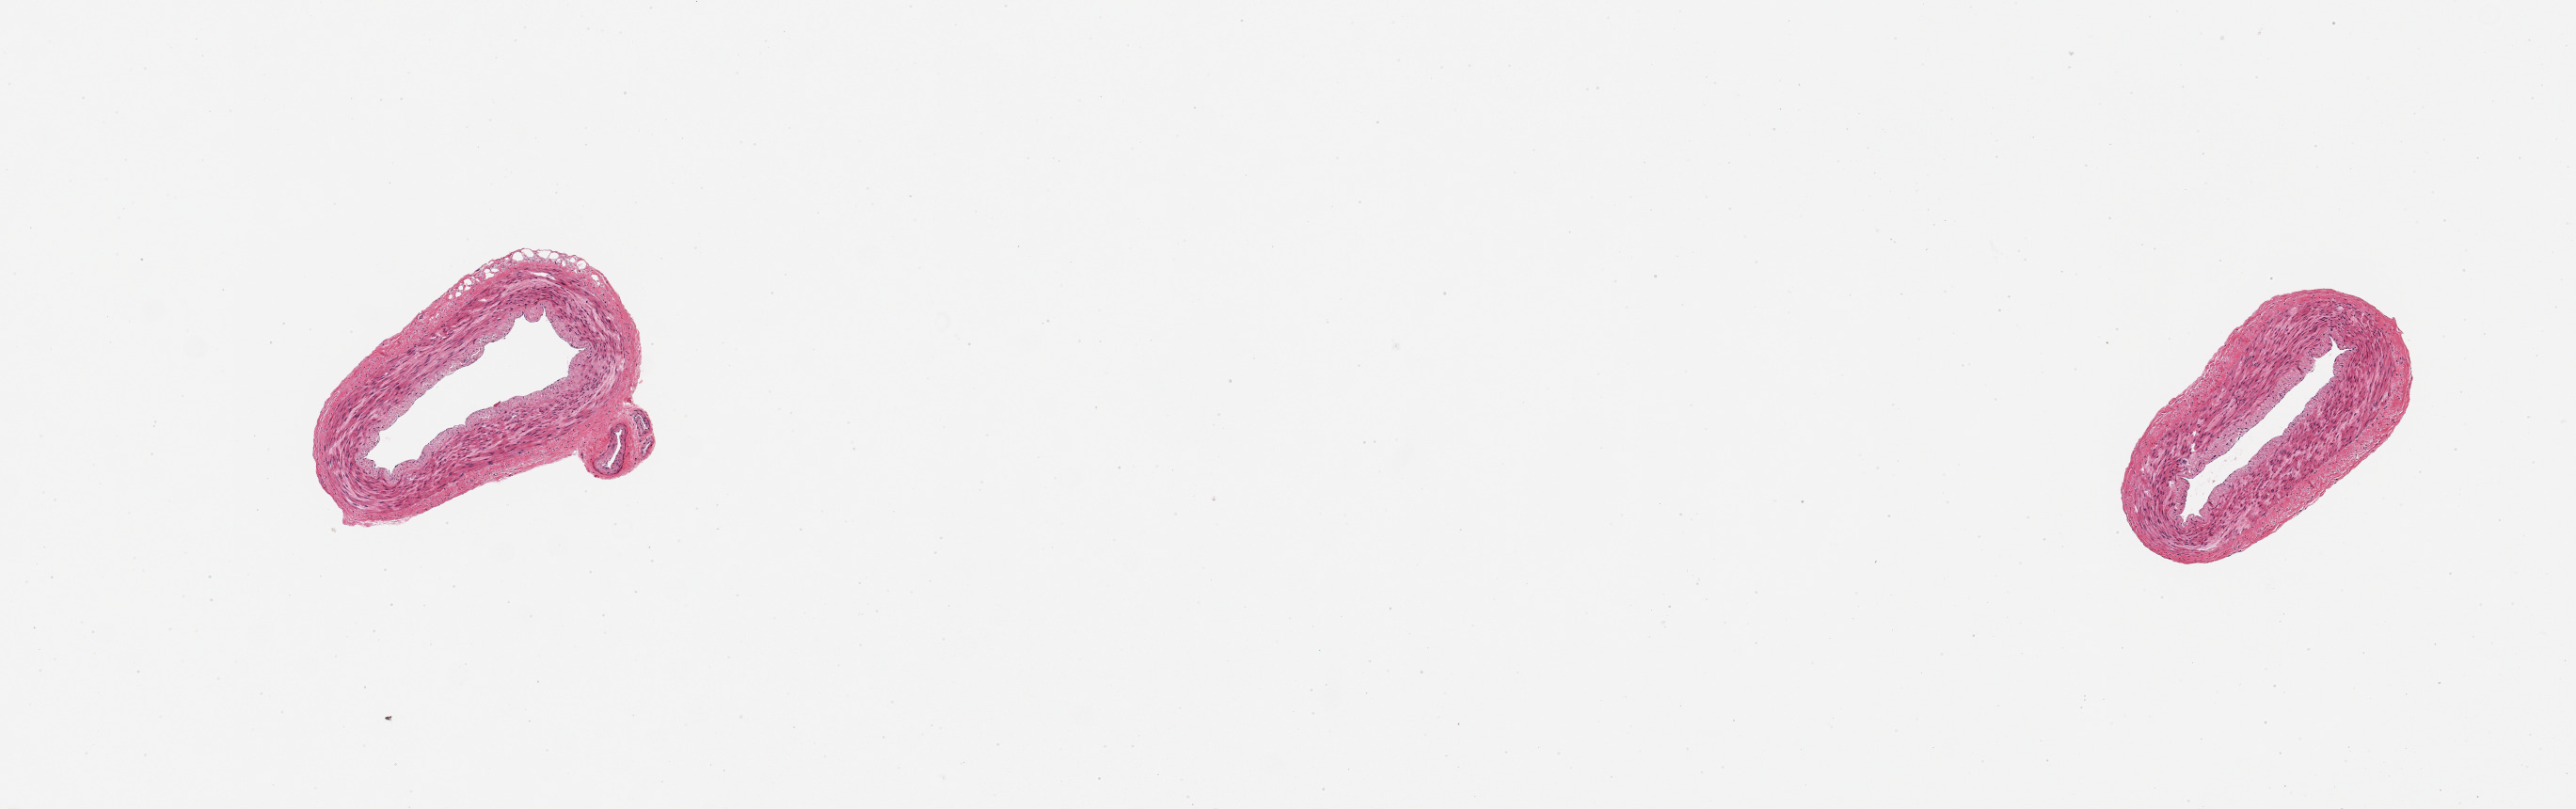
Hematoxylin and eosin (H&E) whole-slide image, whole scanned area (about 10.8 x 3.4 mm) shown as a low-resolution overview, PAXgene-fixed paraffin-embedded (PFPE) section, sampled site (target tissue): tibial artery, donor tissue sample.
Pathologist's review note for this sample: 2 pieces; no lesions; well trimmed.